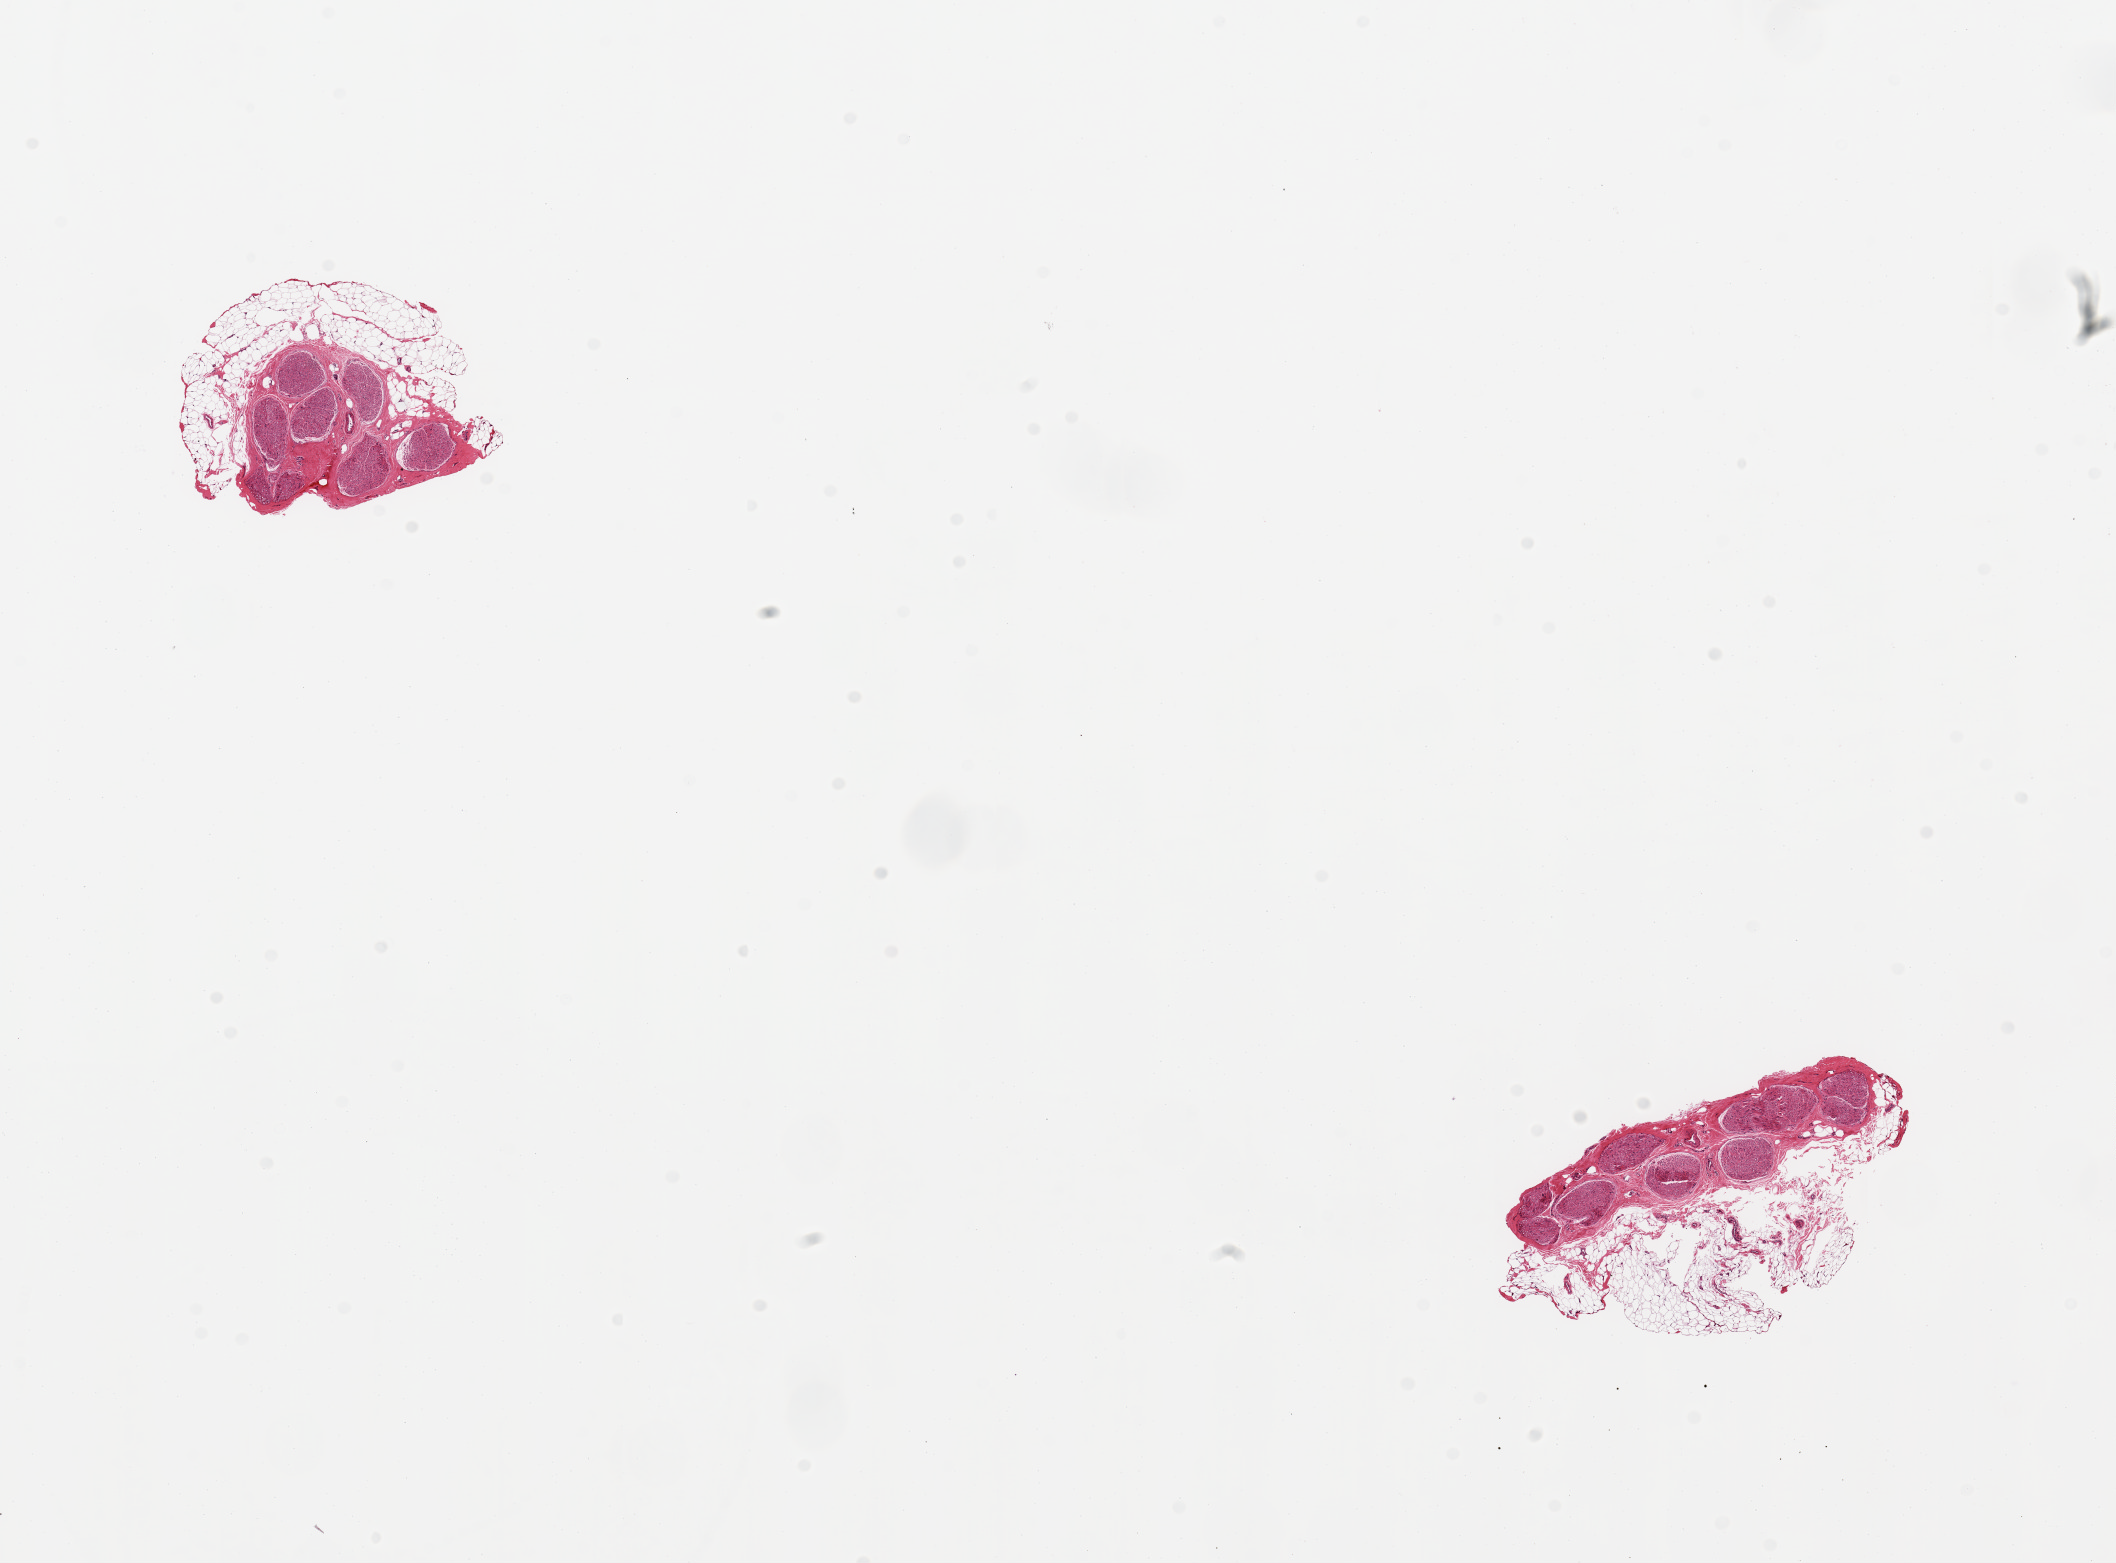
Digitized haematoxylin and eosin-stained section — a low-resolution overview of the entire scanned area, about 16.7 x 12.4 mm, PAXgene-fixed paraffin-embedded (PFPE) section, section of tibial nerve (target tissue), tissue donor sample. Donor sex: male.
Pathologist's review note for this sample: 2 ~ 2.5x1mm nerve pieces; attached fat is ~ 50% of each aliquot.